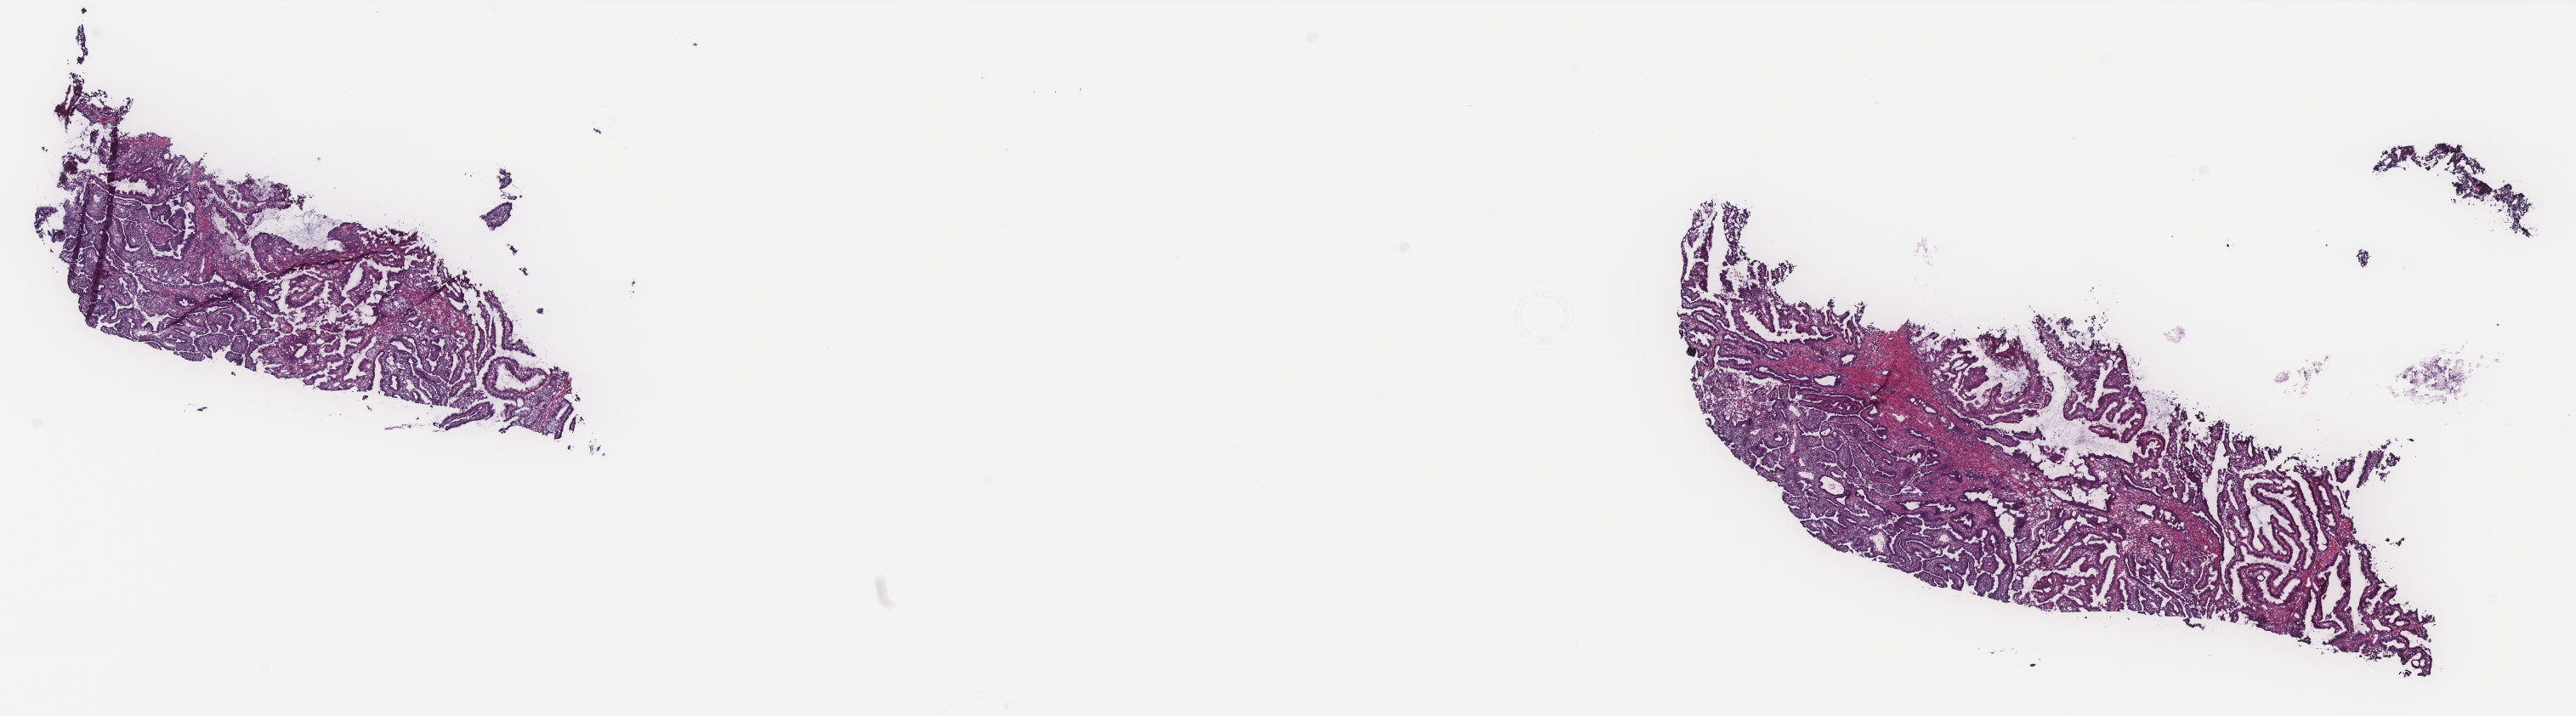
Whole-slide histology image, H&E-stained, whole scanned area (about 24.3 x 6.8 mm) shown as a low-resolution overview, frozen section from the top of the tissue portion, sample: primary tumour, cervix. Female, age 40 years at initial diagnosis. Histologic grade: G1 (well differentiated). Slide review estimates, as recorded: tumour cells 60%, tumour nuclei 60%, normal cells 0%, stromal cells 40%, necrosis 0%. Inflammatory infiltration, as recorded: lymphocyte infiltration 15%, monocyte infiltration 0%, neutrophil infiltration 5%.
Lymph nodes positive (case pathology): 0 of 27 examined. Histologic diagnosis: Adenocarcinoma, NOS. FIGO stage: IB1.